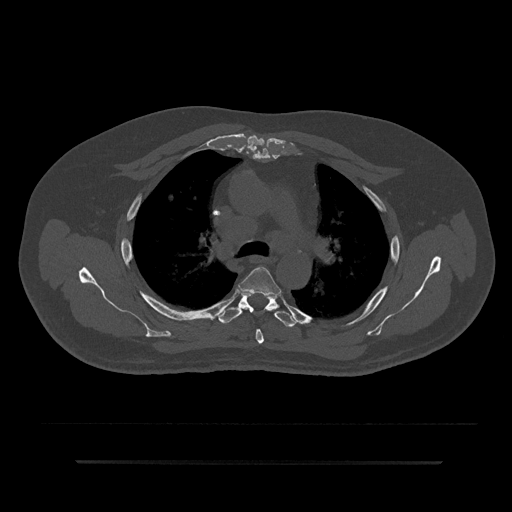
CT including the spine, one axial slice. Position 596 of 797 along the scan axis. Reconstruction kernel Br40s/3. 120 kVp. Bone window (W 1800 / L 400 HU). 0.5 mm slice thickness. 512 × 512 image matrix, field of view 464 × 464 mm. Patient: male, 59 years. Case-level facts recorded for this patient, not image findings: primary cancer: bile ducts; vertebrae with lytic lesions (as recorded): T10.
Outlined on this slice (semi-automatically segmented with operator editing):
- T4 vertebra: bounding box [x1, y1, x2, y2] px = [238, 267, 281, 344]
- T5 vertebra: [219, 293, 297, 327]